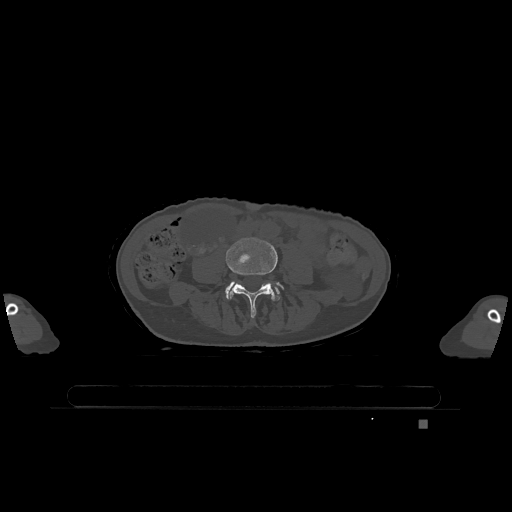
CT including the spine, one axial slice. Bone window (W 1800 / L 400 HU). 512 × 512 image matrix. Female patient, age 74 years. From the clinical record (not read from this slice): primary cancer: lung; vertebrae with lytic lesions (as recorded): T1, T4, T5, T6, L4, L5.
Outlined on this slice (semi-automatic segmentation, software-assisted and operator-edited):
- L4 vertebra: bounding box <226,237,284,318> (left, top, right, bottom; pixels)
- L5 vertebra: <225,284,280,300>